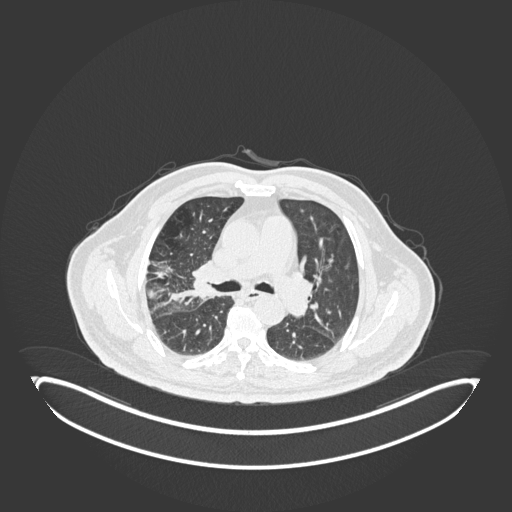
Chest CT, one axial slice; position 106 of 247 along the scan axis; reconstruction kernel B30f; 120 kVp; lung window (W 1500 / L -600 HU); 1 mm slice thickness; 512 × 512 image matrix, field of view 500 × 500 mm. Male patient, age 72 years. From the clinical record (not read from this slice): clinical TNM (as recorded): T1c N0 M0; histopathological grade: G2.
Structures marked on this image (bounding box drawn by a radiologist):
- lung tumour (recorded histology: squamous cell carcinoma): bounding box [x1, y1, x2, y2] px = [178, 266, 222, 302]